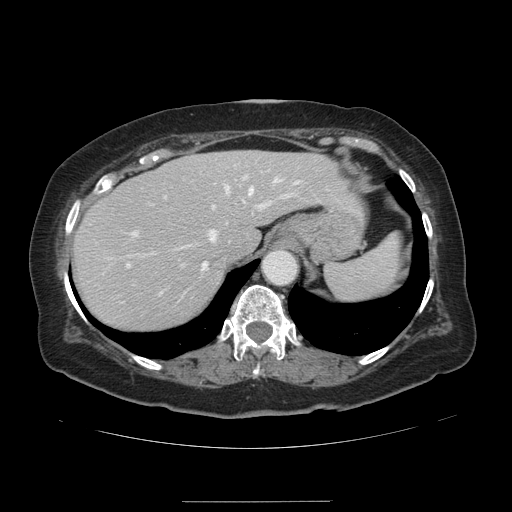
Contrast-enhanced abdominal CT, one axial slice. Position 102 of 141 along the scan axis. 120 kVp. Intravenous contrast given. Soft-tissue window (W 400 / L 40 HU). 2.5 mm slice thickness. 512 × 512 image matrix, field of view 393 × 393 mm. Female patient, age 74 years. From the clinical record (not read from this slice): diagnosis: colorectal cancer liver metastases, imaged before liver resection; multiple liver metastases: yes; largest metastasis: 7 cm; disease in both lobes: yes.
Annotated regions visible in this slice (manually delineated by an expert):
- hepatic veins: bounding box [x1, y1, x2, y2] px = [106, 178, 298, 299]
- liver: [73, 151, 362, 332]
- planned liver remnant (the part of the liver to remain after resection): [73, 151, 362, 332]
- portal vein (with intrahepatic branches): [127, 175, 290, 294]